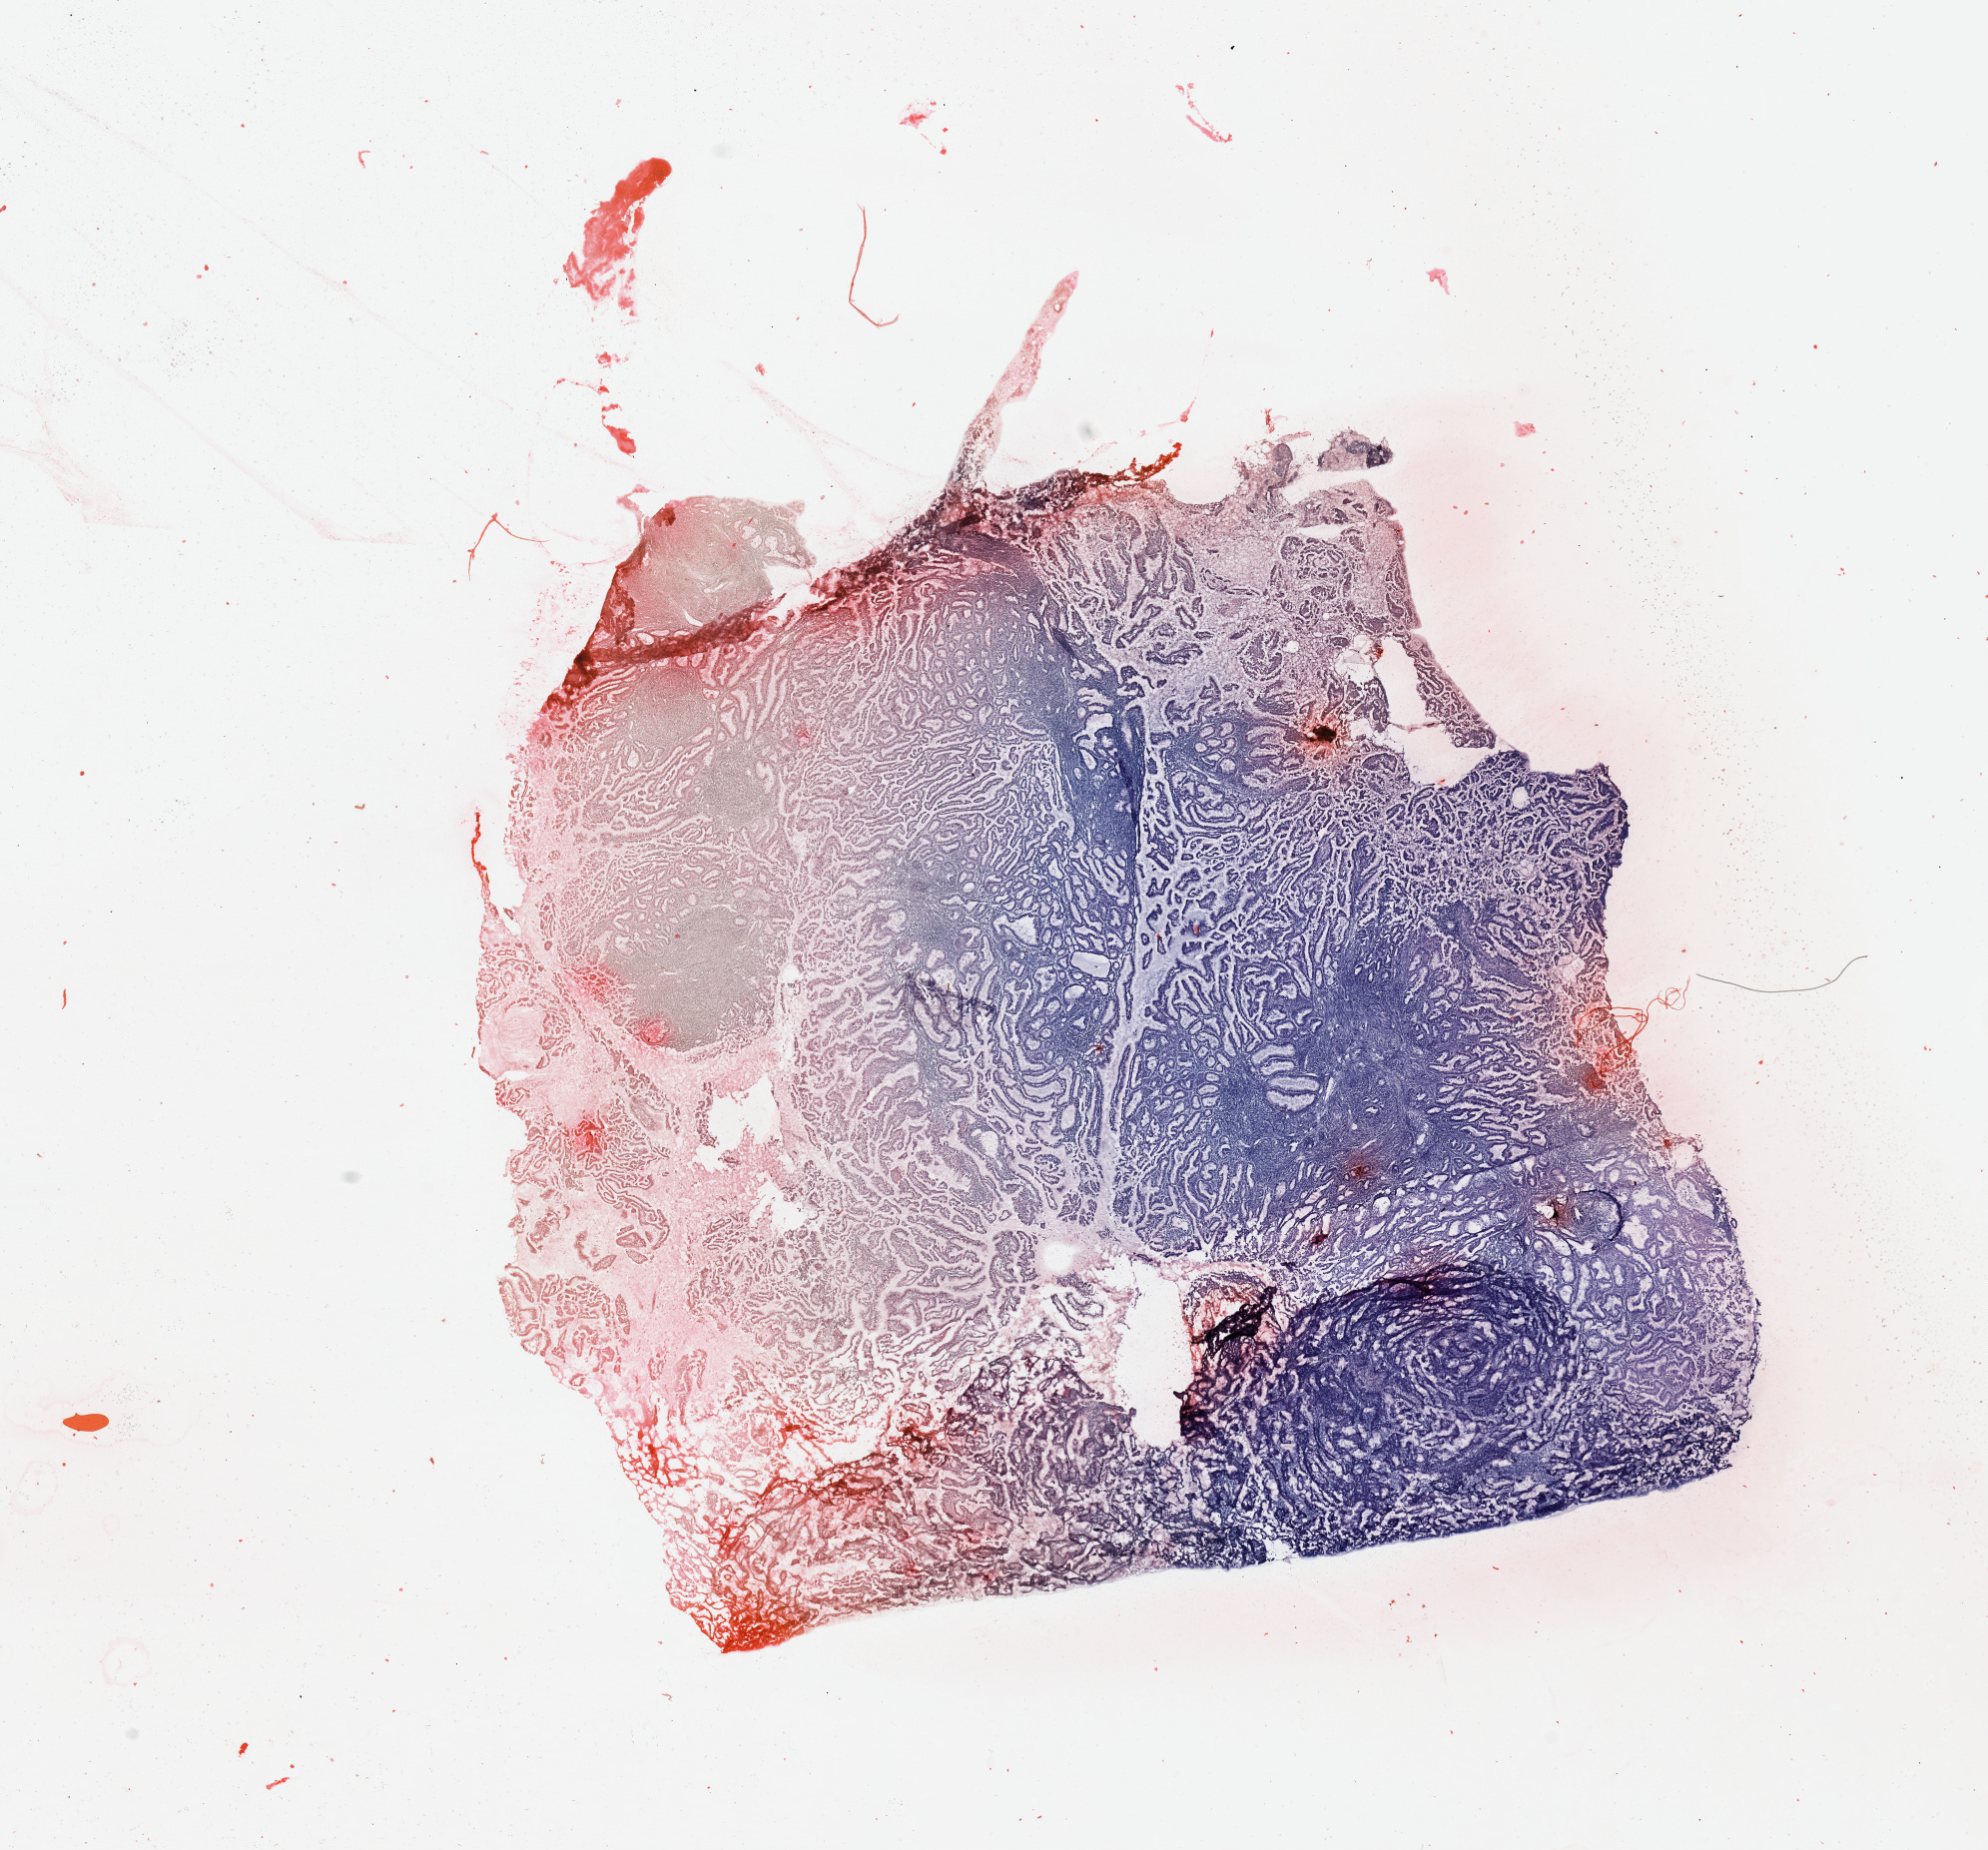
Digitized Hematoxylin and eosin (H&E) stained tissue section (whole slide) — shown as a low-resolution overview of the whole scanned area (about 15.8 x 14.7 mm, slide scanned at 20x), uterus, tumour tissue. Patient: female, age 61 years. Histologic grade: G1 (well differentiated).
* histologic diagnosis: Endometrioid adenocarcinoma, NOS
* AJCC pathologic stage: I